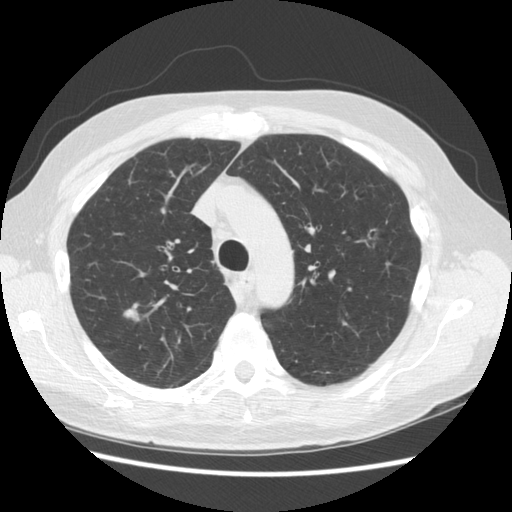
Low-dose screening chest CT, axial slice, third screening round (two years after baseline), lung window (W 1500 / L -600 HU), 2.5 mm slice thickness, standard (soft-tissue) reconstruction kernel (STANDARD), 512 × 512 image matrix, field of view 360 × 360 mm. Male participant, aged 68 years at enrolment.
Lesion marked by an expert reader, box from (x=108, y=297) to (x=153, y=335) px. Screening reader's record for this exam (one nodule recorded; not confirmed to be the boxed lesion): non-calcified nodule or mass ≥4 mm, right upper lobe, 11 × 9 mm, smooth margins, soft tissue attenuation, pre-existing on the prior screen: yes; interval growth: yes. Lung cancer was diagnosed 246 days after this screen: adenocarcinoma, NOS, right upper lobe, moderately differentiated (G2), stage IA (AJCC 6th edition), 13 mm at pathology.